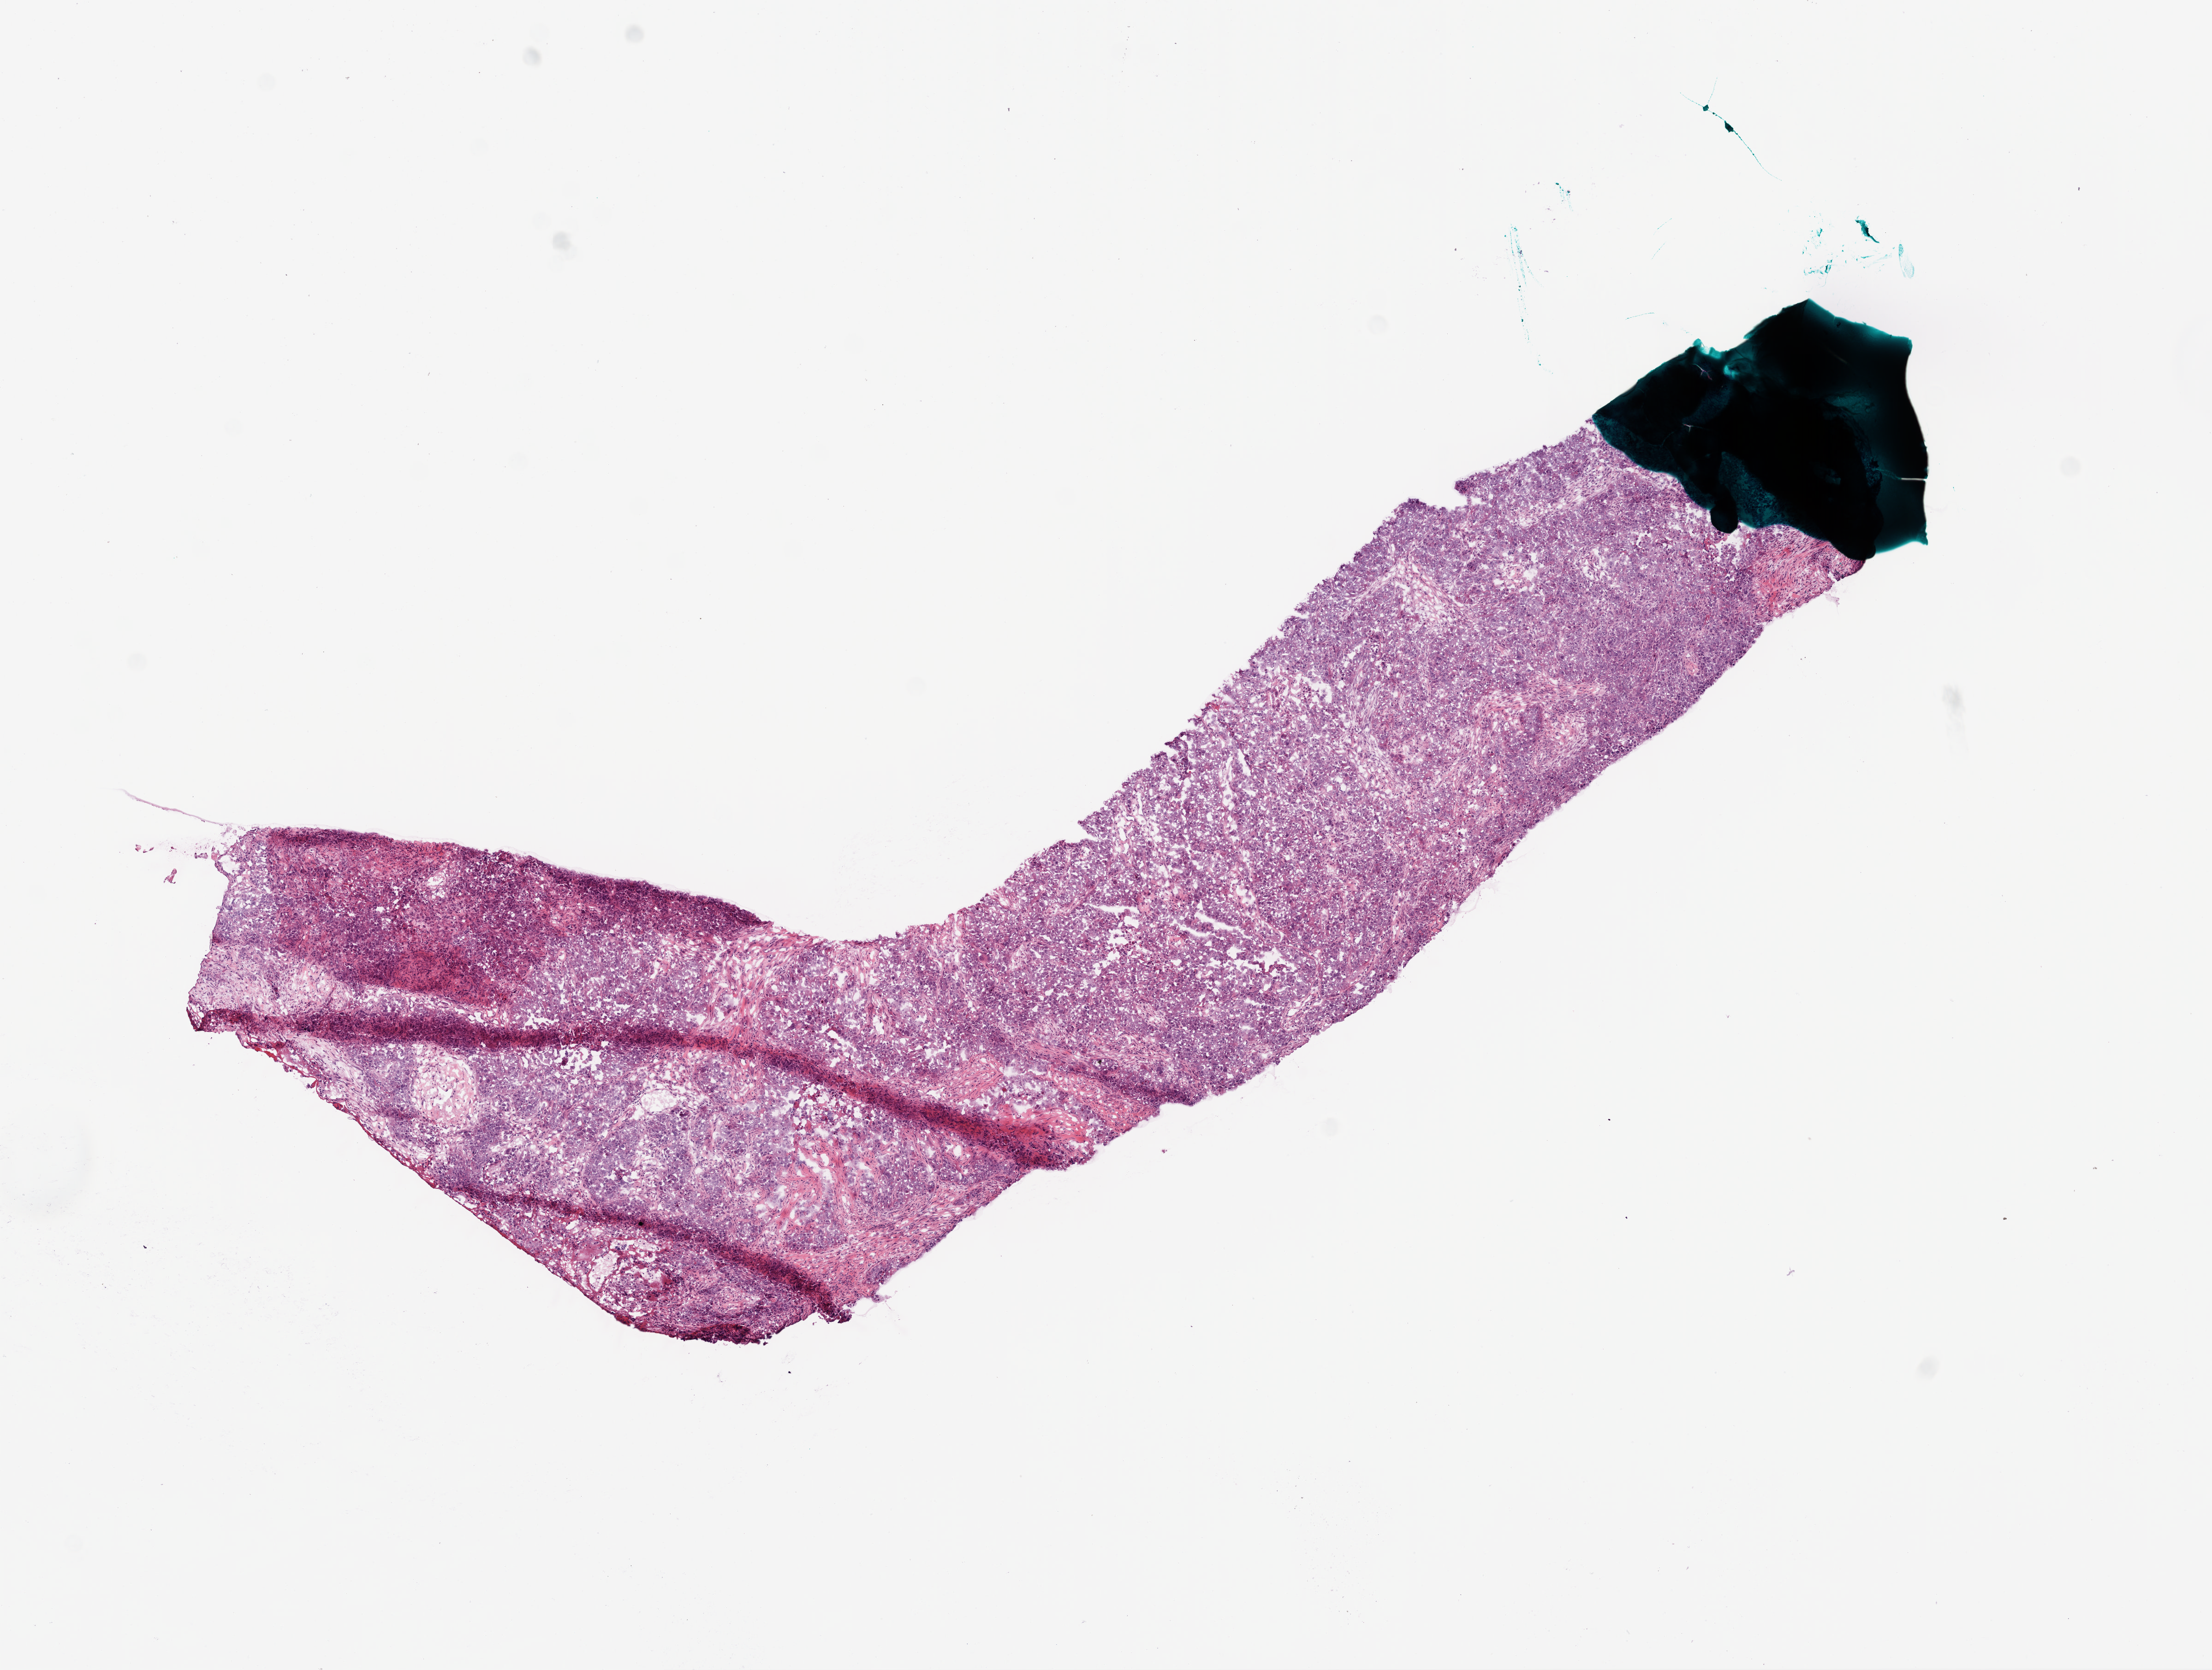
Digitized Hematoxylin and eosin (H&E) stained tissue section (whole slide), a low-resolution overview of the entire scanned area, about 9.7 x 7.3 mm (slide scanned at 20x), frozen section, primary tumour sample from the ovary. Female, age 70 years at initial diagnosis. Histologic grade: G3 (poorly differentiated). Pathologist review of this section (percent, as recorded): tumour cells 95%, tumour nuclei 98%, normal cells 0%, stromal cells 5%, necrosis 0%.
FIGO stage: IIIC. Histologic diagnosis: Serous cystadenocarcinoma, NOS.